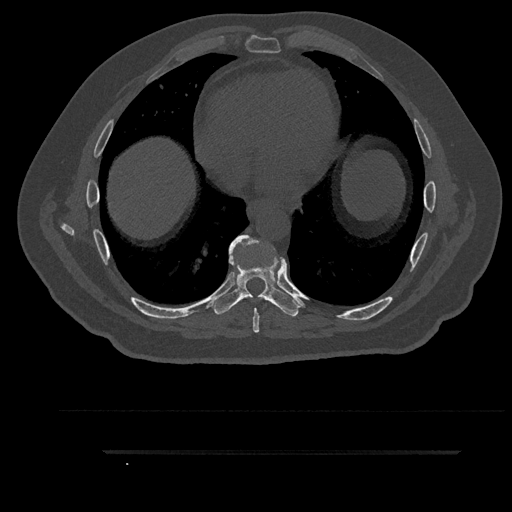
CT including the spine, one axial slice; position 494 of 797 along the scan axis; reconstruction kernel Br40s/3; bone window (W 1800 / L 400 HU); 0.5 mm slice thickness; 512 × 512 image matrix, field of view 432 × 432 mm. Patient: male, 63 years. Case-level facts recorded for this patient, not image findings: primary cancer: renal; vertebrae with lytic lesions (as recorded): T8.
Outlined on this slice (semi-automatically segmented with operator editing):
- T7 vertebra: bounding box [x1, y1, x2, y2] px = [236, 236, 284, 333]
- T8 vertebra: [211, 235, 300, 317]